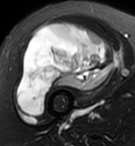
MRI of an extremity soft-tissue mass, one axial slice; position 60 of 95 along the scan axis; T2-weighted fat-saturated; MR volume resampled by the dataset authors to the PET/CT grid (not the native acquisition matrix); 3.27 mm slice thickness; 135 × 146 image matrix, field of view 132 × 143 mm. Female patient. Case-level facts recorded for this patient, not image findings: histological type: pleiomorphic undifferentiated sarcoma; grade: high; site of the primary tumour: right quadricep.
Structures marked on this image (expert contour drawn on MRI and transferred to this co-registered scan by the dataset authors):
- gross tumour volume including surrounding oedema: bounding box (x1, y1, x2, y2) in pixels: (16, 22, 116, 117)
- gross tumour volume (mass): (16, 22, 116, 117)